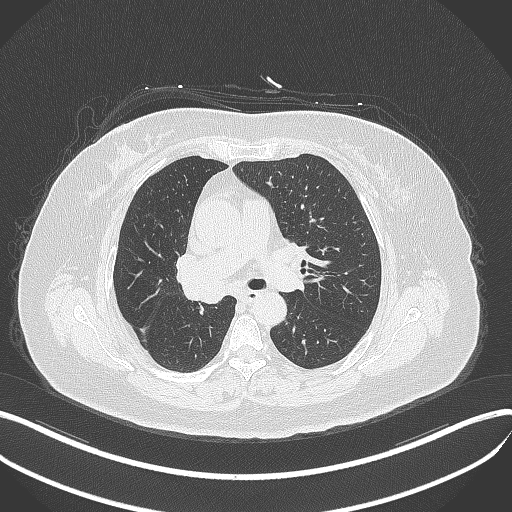
Chest CT, one axial slice; slice 217 of 376 in the series (ordered by position); reconstruction kernel B70f; lung window (W 1500 / L -600 HU); 1 mm slice thickness; 512 × 512 image matrix. Patient: female, 60 years. From the clinical record (not read from this slice): clinical TNM (as recorded): T1c N0 M0; histopathological grade: G1-G2.
Structures marked on this image (bounding box drawn by a radiologist):
- lung tumour (recorded histology: squamous cell carcinoma): bounding box [x1, y1, x2, y2] px = [180, 272, 229, 306]